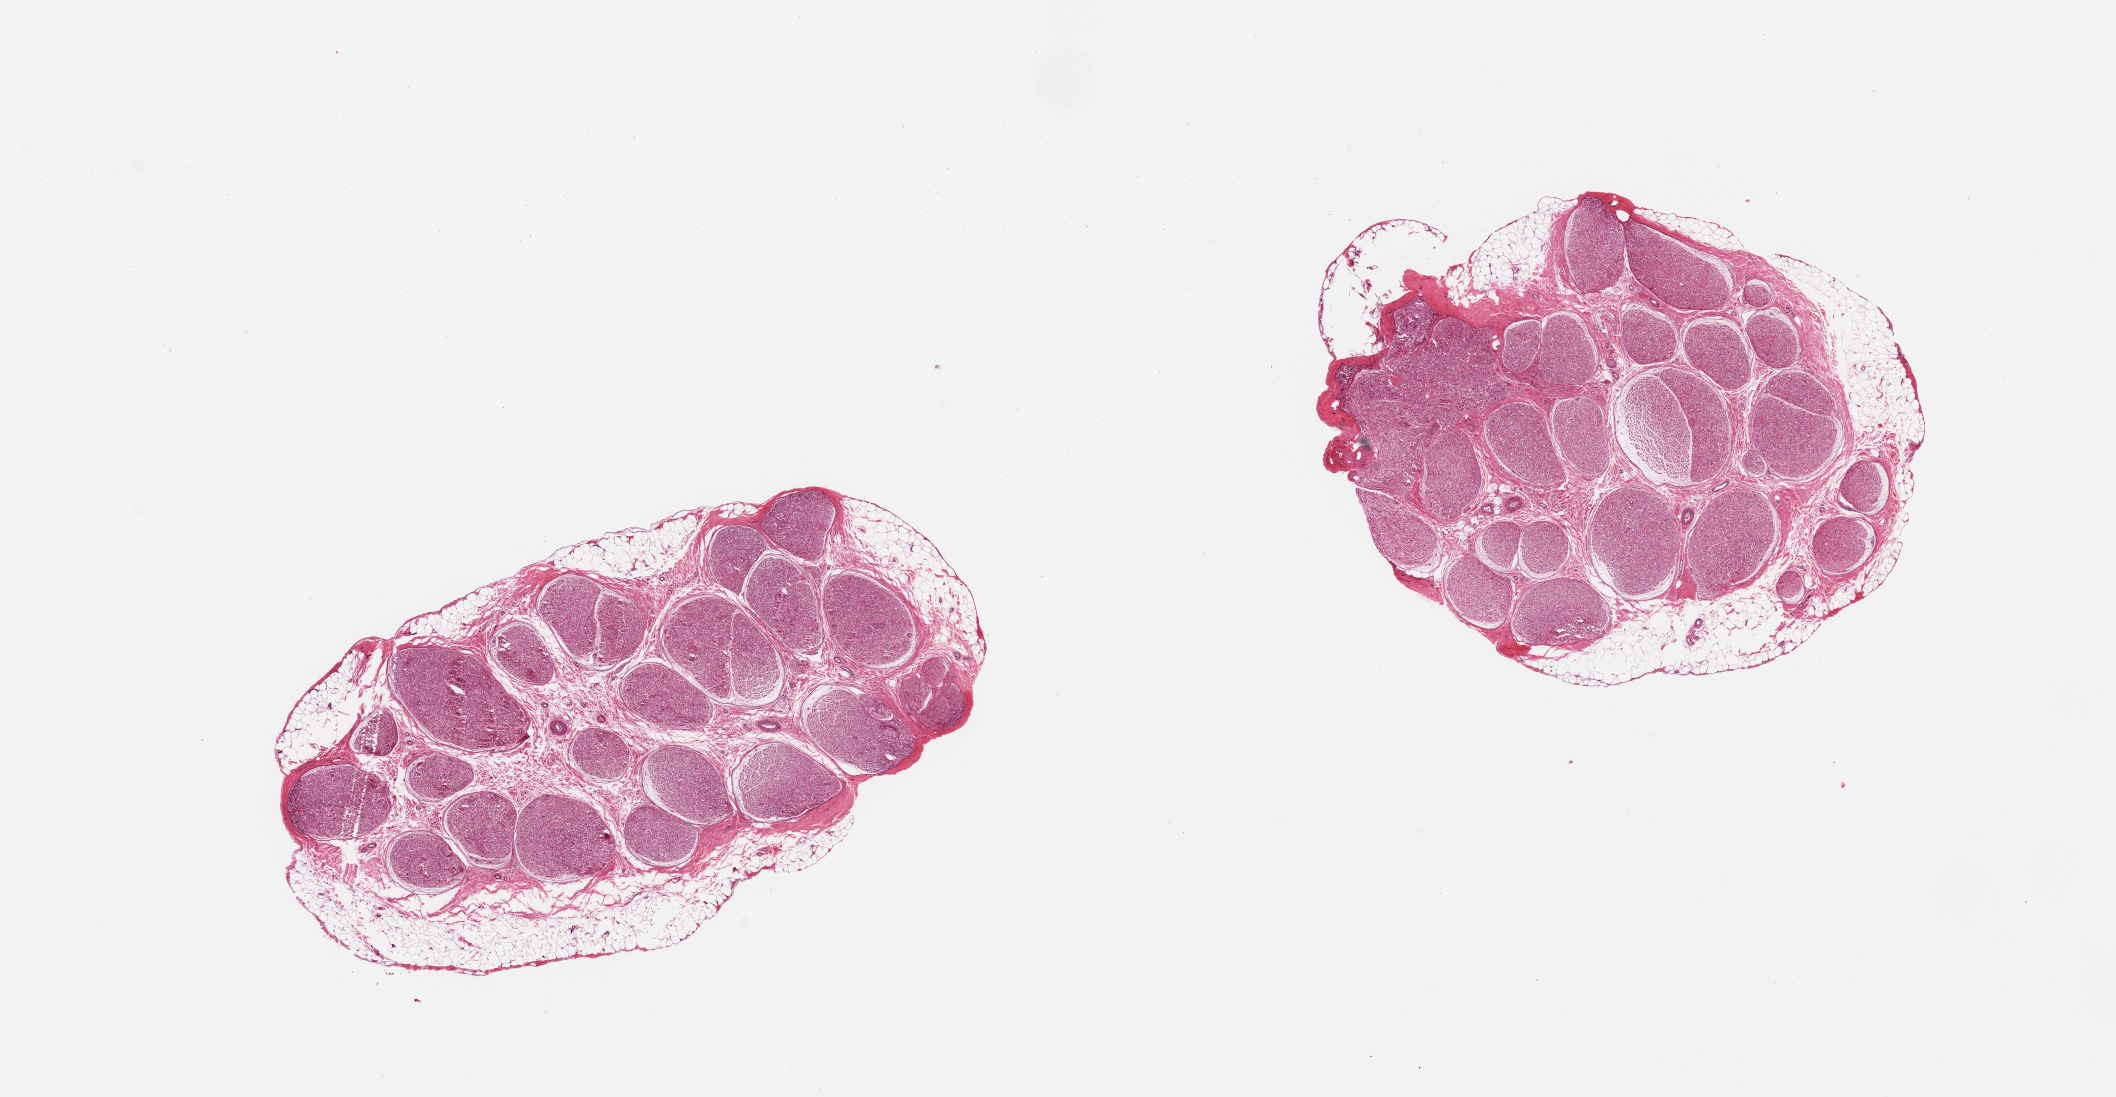
Hematoxylin and eosin (H&E) whole-slide image — whole scanned area (about 16.7 x 8.7 mm, slide scanned at 20x) shown as a low-resolution overview, PAXgene-fixed paraffin-embedded (PFPE) section, section of tibial nerve (target tissue), donor tissue sample. Donor: female.
Review note (as recorded): 2 pieces; up to 0.7mm rim of fat.